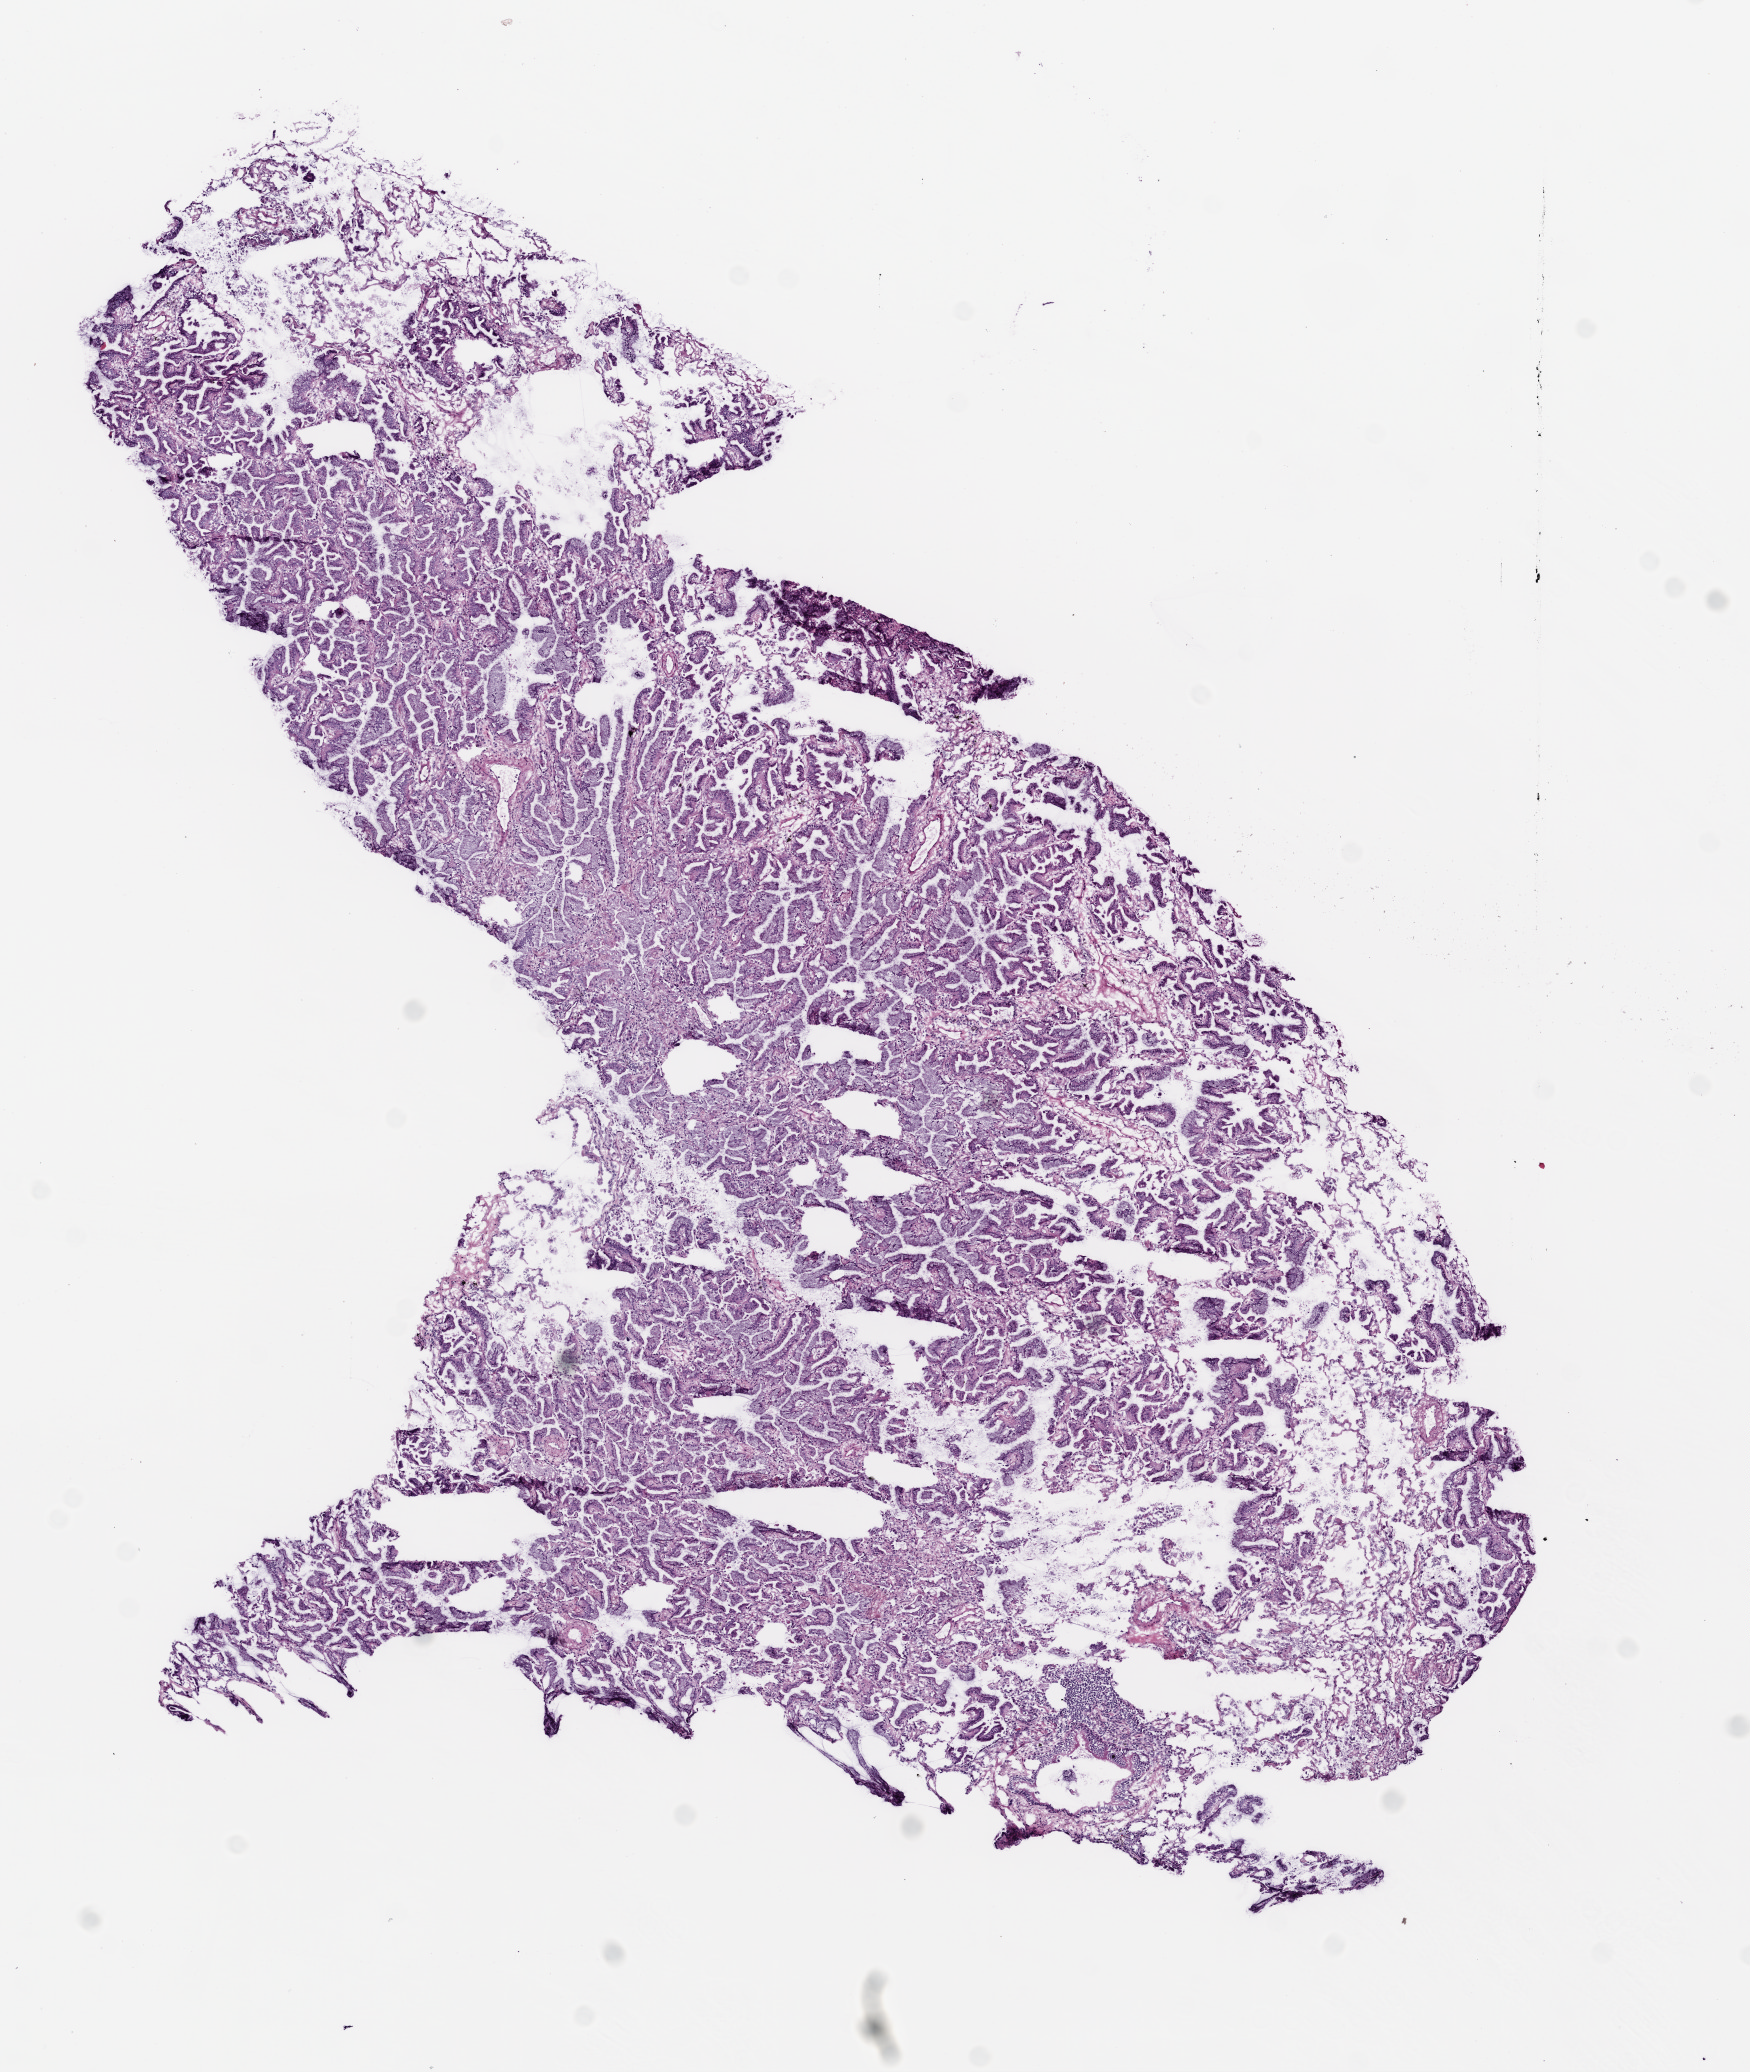
Whole-slide histology image, Hematoxylin and eosin (H&E) stained — low-resolution overview of the scanned area, about 7.0 x 8.3 mm (from a 20x scan); frozen section; primary tumour sample from the lung. Male patient; age at initial diagnosis 76 years. Slide review estimates, as recorded: tumour cells 80%, tumour nuclei 75%, normal cells 5%, stromal cells 20%, necrosis 0%.
TNM: T2 N0 M0. AJCC pathologic stage: IB (5th edition). Histologic diagnosis: Adenocarcinoma with mixed subtypes (upper lobe, lung).